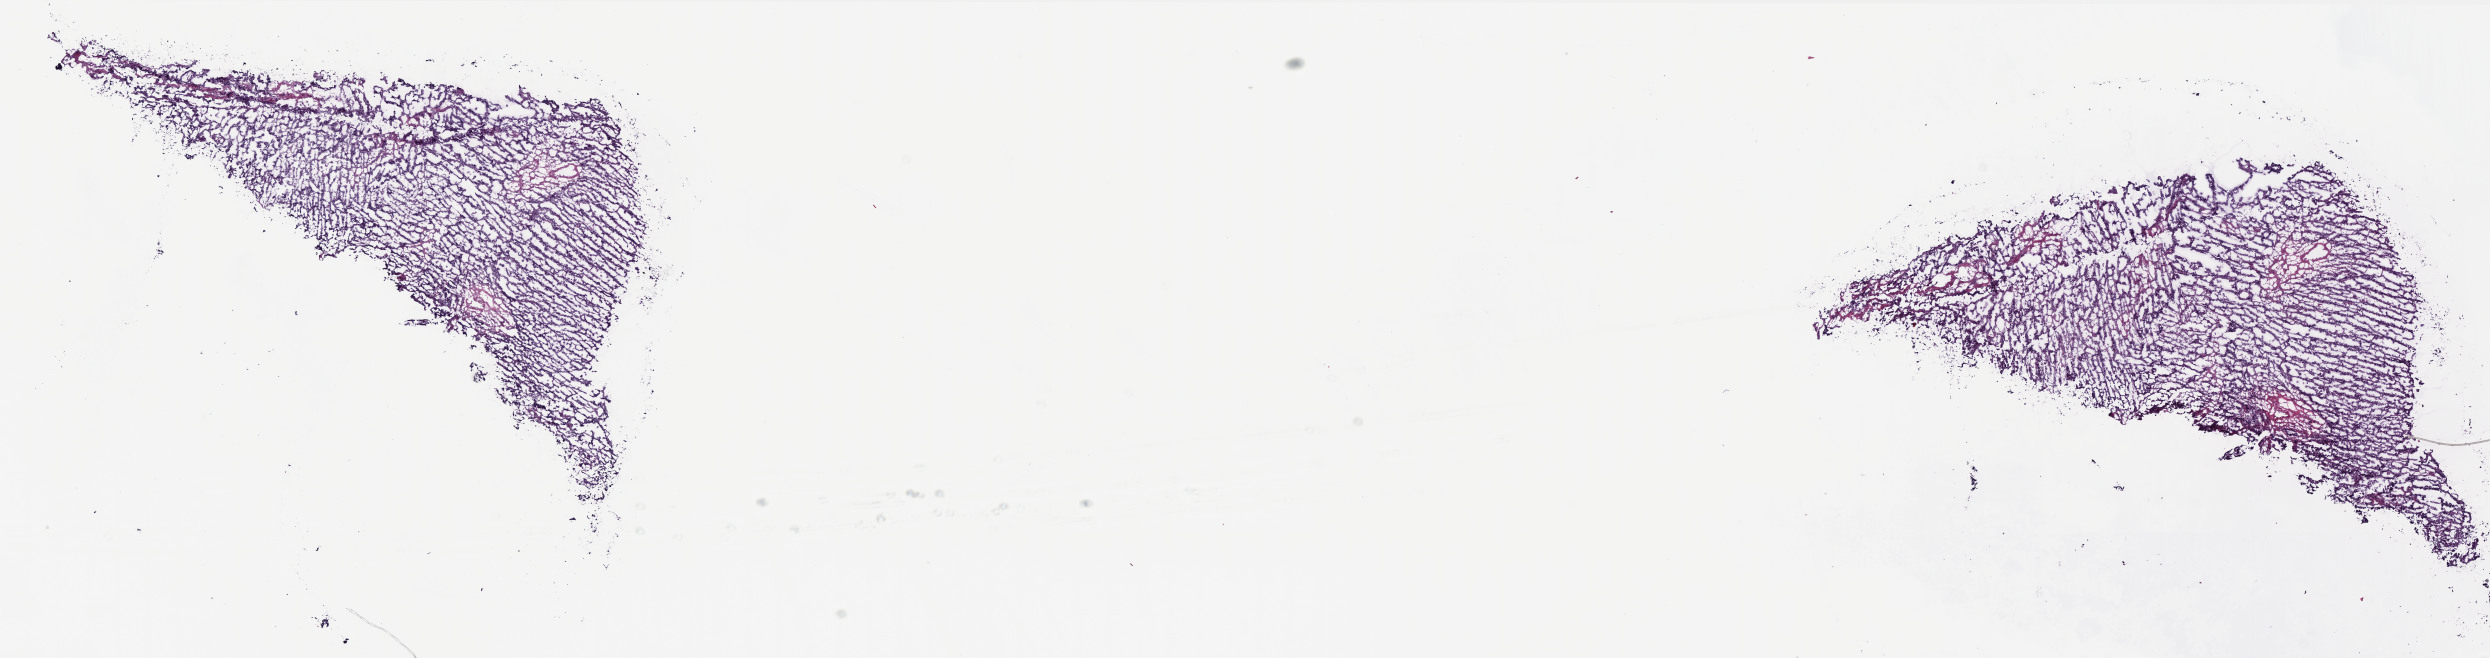
Digitized H&E tissue section (whole slide) — a low-resolution overview of the entire scanned area, about 20.0 x 5.3 mm. Frozen section. Primary tumour sample from the uterus. Female patient; age at initial diagnosis 67 years. Histologic grade: G3 (poorly differentiated). Slide review estimates, as recorded: tumour cells 79%, tumour nuclei 70%, normal cells 0%, stromal cells 20%, necrosis 1%. Infiltration values recorded for this section: lymphocyte infiltration 10%, monocyte infiltration 0%, neutrophil infiltration 0%.
FIGO stage: IIIC2. Lymph nodes positive (case pathology): 1 of 29 examined. Pathologic diagnosis: Serous cystadenocarcinoma, NOS (endometrium).